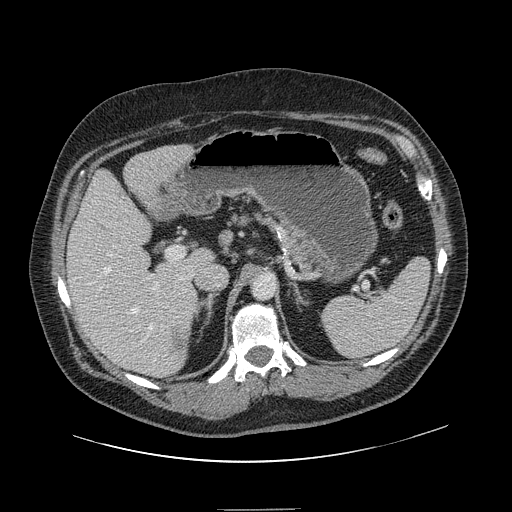
Contrast-enhanced abdominal CT, one axial slice; slice 86 of 154 in the series (ordered by position); 120 kVp; intravenous contrast given; soft-tissue window (W 400 / L 40 HU); 2.5 mm slice thickness; 512 × 512 image matrix, field of view 451 × 451 mm. Male patient, age 61 years. From the clinical record (not read from this slice): diagnosis: colorectal cancer liver metastases, imaged before liver resection; multiple liver metastases: yes; largest metastasis: 2.6 cm; disease in both lobes: yes.
Structures marked on this image (manually delineated by an expert):
- hepatic veins: bounding box (x1, y1, x2, y2) in pixels: (103, 245, 156, 361)
- liver: (68, 145, 212, 377)
- planned liver remnant (the part of the liver to remain after resection): (69, 148, 212, 366)
- portal vein (with intrahepatic branches): (98, 254, 159, 291)
- liver metastasis: (172, 334, 189, 356)